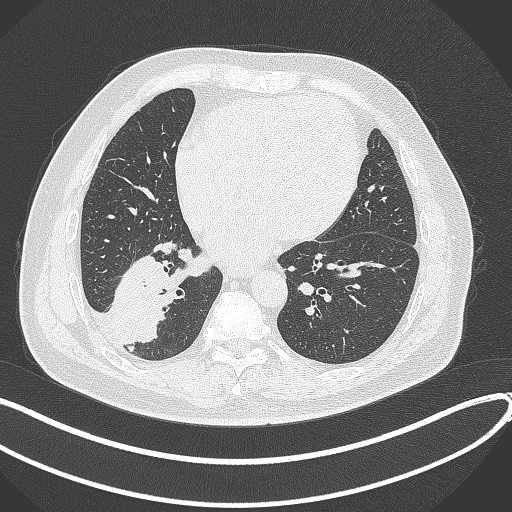
Chest CT, one axial slice. Position 131 of 360 along the scan axis. Reconstruction kernel B70f. Lung window (W 1500 / L -600 HU). 512 × 512 image matrix. Male patient, age 59 years.
Outlined on this slice (rectangle marked by the reading radiologist):
- lung tumour (recorded histology: adenocarcinoma): bounding box [x1, y1, x2, y2] px = [108, 249, 176, 346]